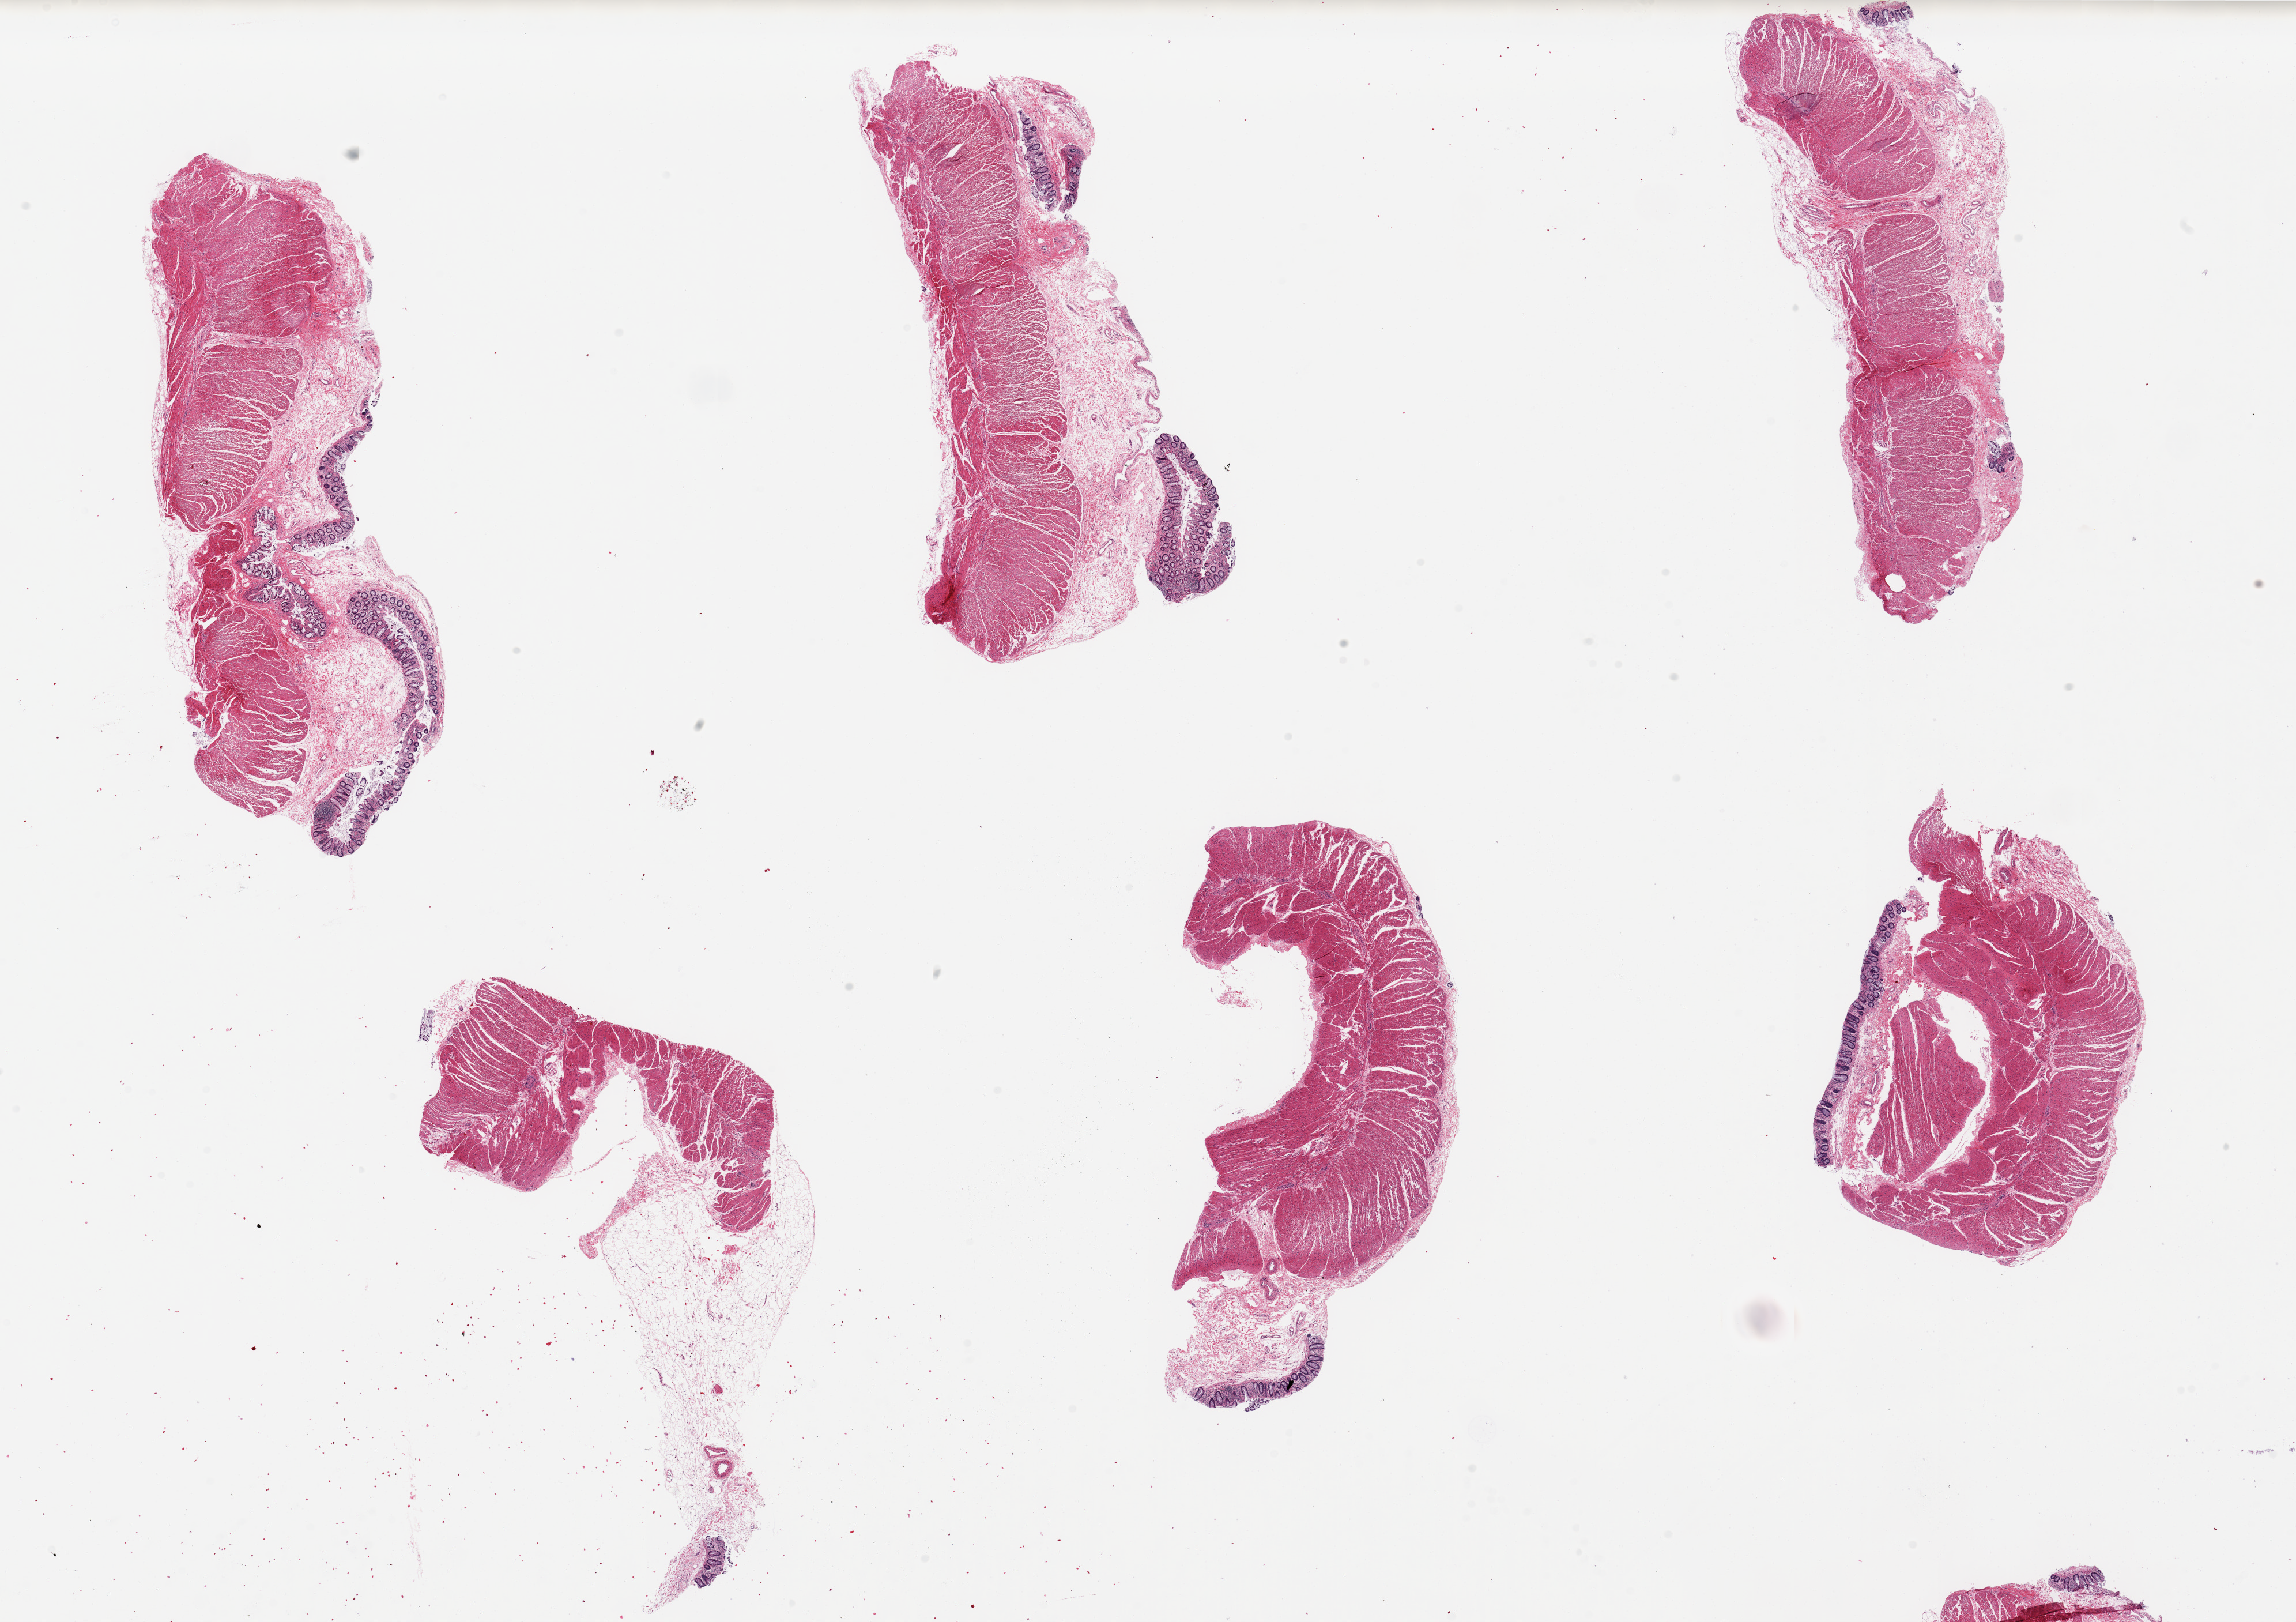
Whole-slide image, H&E stain, shown as a low-resolution overview of the whole scanned area (about 31.5 x 22.2 mm, from a 20x scan). PAXgene-fixed, paraffin-embedded tissue. Target tissue: sigmoid colon. Tissue donor sample. Male donor.
Reviewer comment on this tissue sample: 6 pieces, up to 10x4mm; All pieces have mucosa and variable amounts of submucosal adipose. The sigmoid colon target is muscle only.